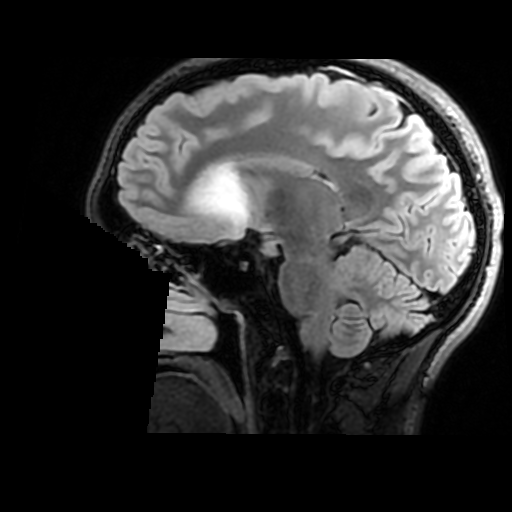
Brain MRI from a brain-tumour surgery series, one sagittal slice. Position 98 of 176 along the scan axis. T2 FLAIR. 1 mm slice thickness. 512 × 512 image matrix. Case-level facts recorded for this patient, not image findings: histopathology: Astrocytoma; WHO grade: 2; IDH mutation: yes.
Outlined on this slice (outlined manually by an expert reader):
- tumour: bounding box <188,166,249,225> (left, top, right, bottom; pixels)